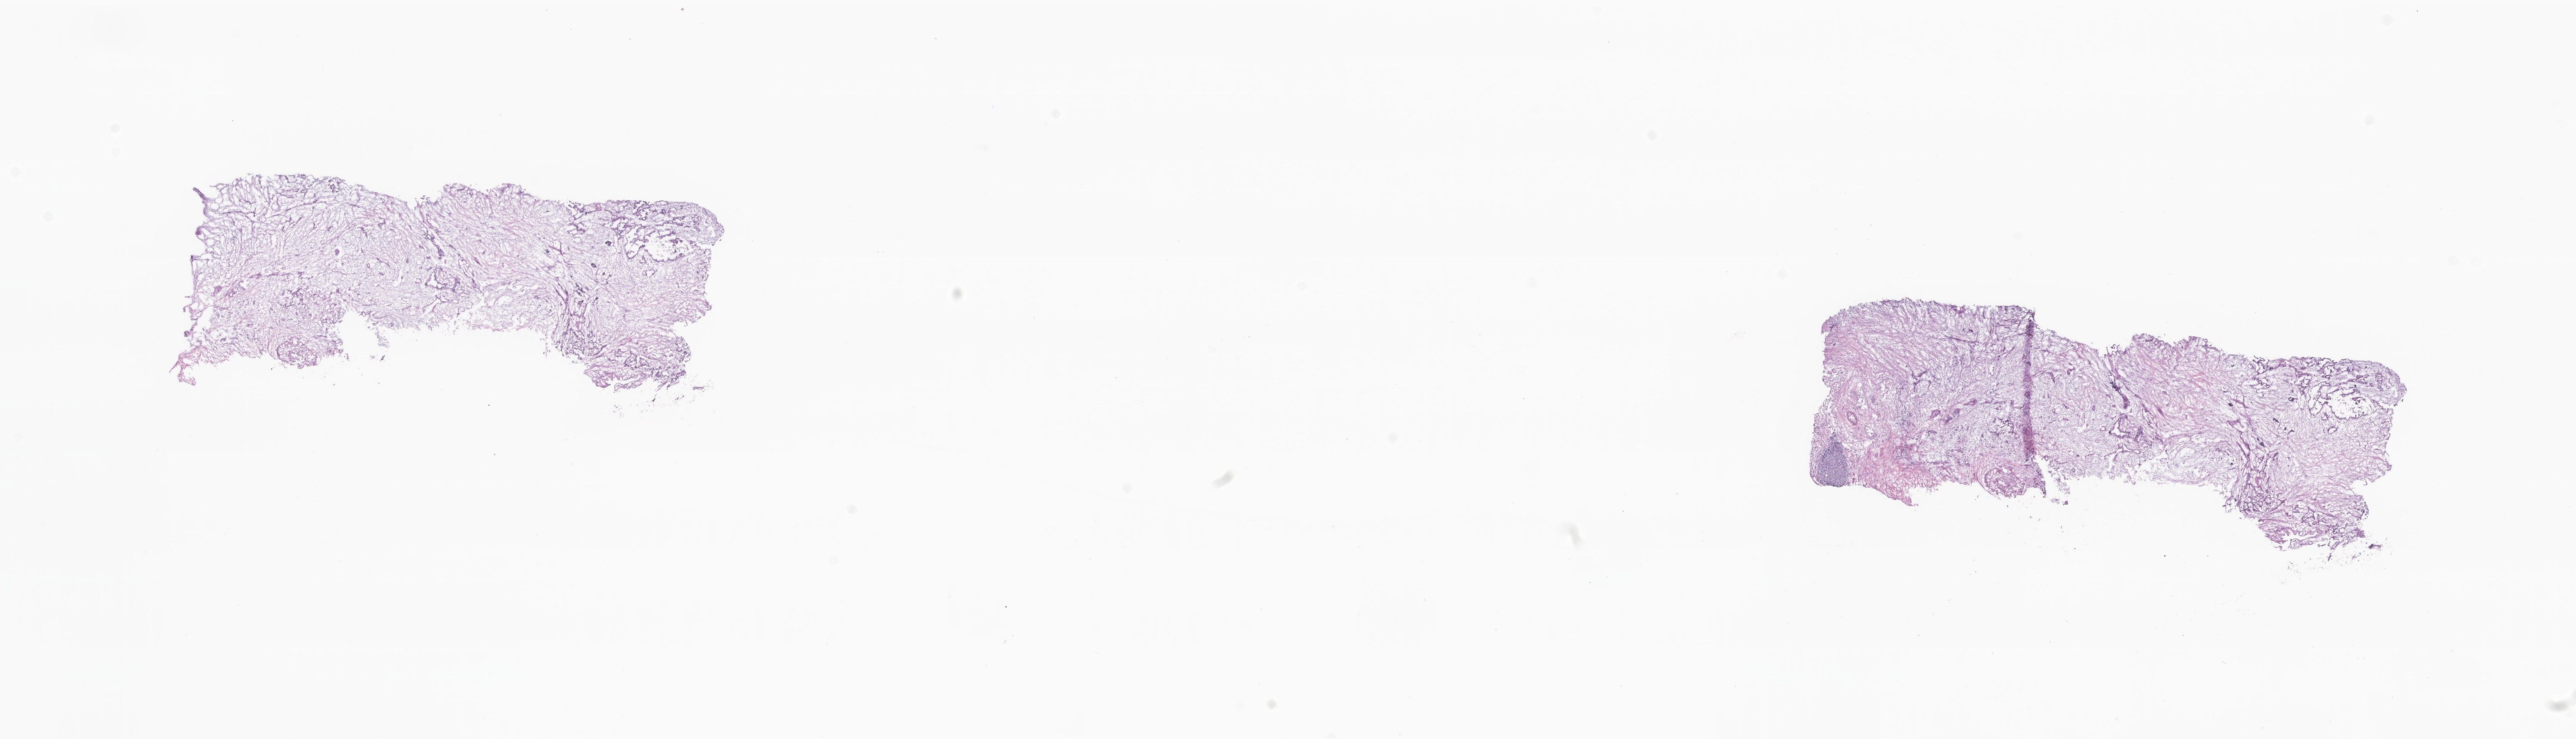
Digitized hematoxylin and eosin (H&E)-stained section — whole scanned area (about 28.2 x 8.1 mm) shown as a low-resolution overview; frozen section (tissue freezing medium); primary tumor; anatomic site: tail of pancreas. Patient: male, age at initial diagnosis 69 years. Slide review estimates, as recorded: tumor cells 30%, tumor nuclei 40%, stromal cells 70%, necrosis 0%, normal cells 0%. Infiltration values recorded for this section: lymphocyte infiltration 0%, monocyte infiltration 0%, neutrophil infiltration 0%.
• diagnosis: Infiltrating duct carcinoma, NOS